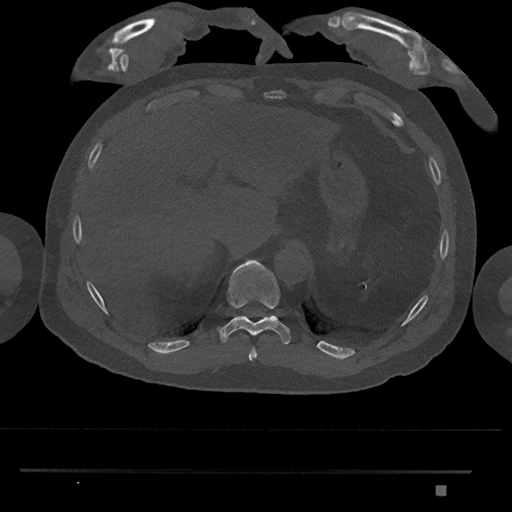
CT including the spine, one axial slice. Slice 999 of 1134 in the series (ordered by position). Reconstruction kernel Br40s/3. 120 kVp. Bone window (W 1800 / L 400 HU). 0.5 mm slice thickness. 512 × 512 image matrix. Patient: male, 65 years. Case-level facts recorded for this patient, not image findings: primary cancer: prostate.
Annotated regions visible in this slice (semi-automatic segmentation, software-assisted and operator-edited):
- T10 vertebra: bounding box (x1, y1, x2, y2) in pixels: (217, 259, 291, 346)
- T11 vertebra: (236, 315, 242, 317)
- T9 vertebra: (248, 347, 257, 361)